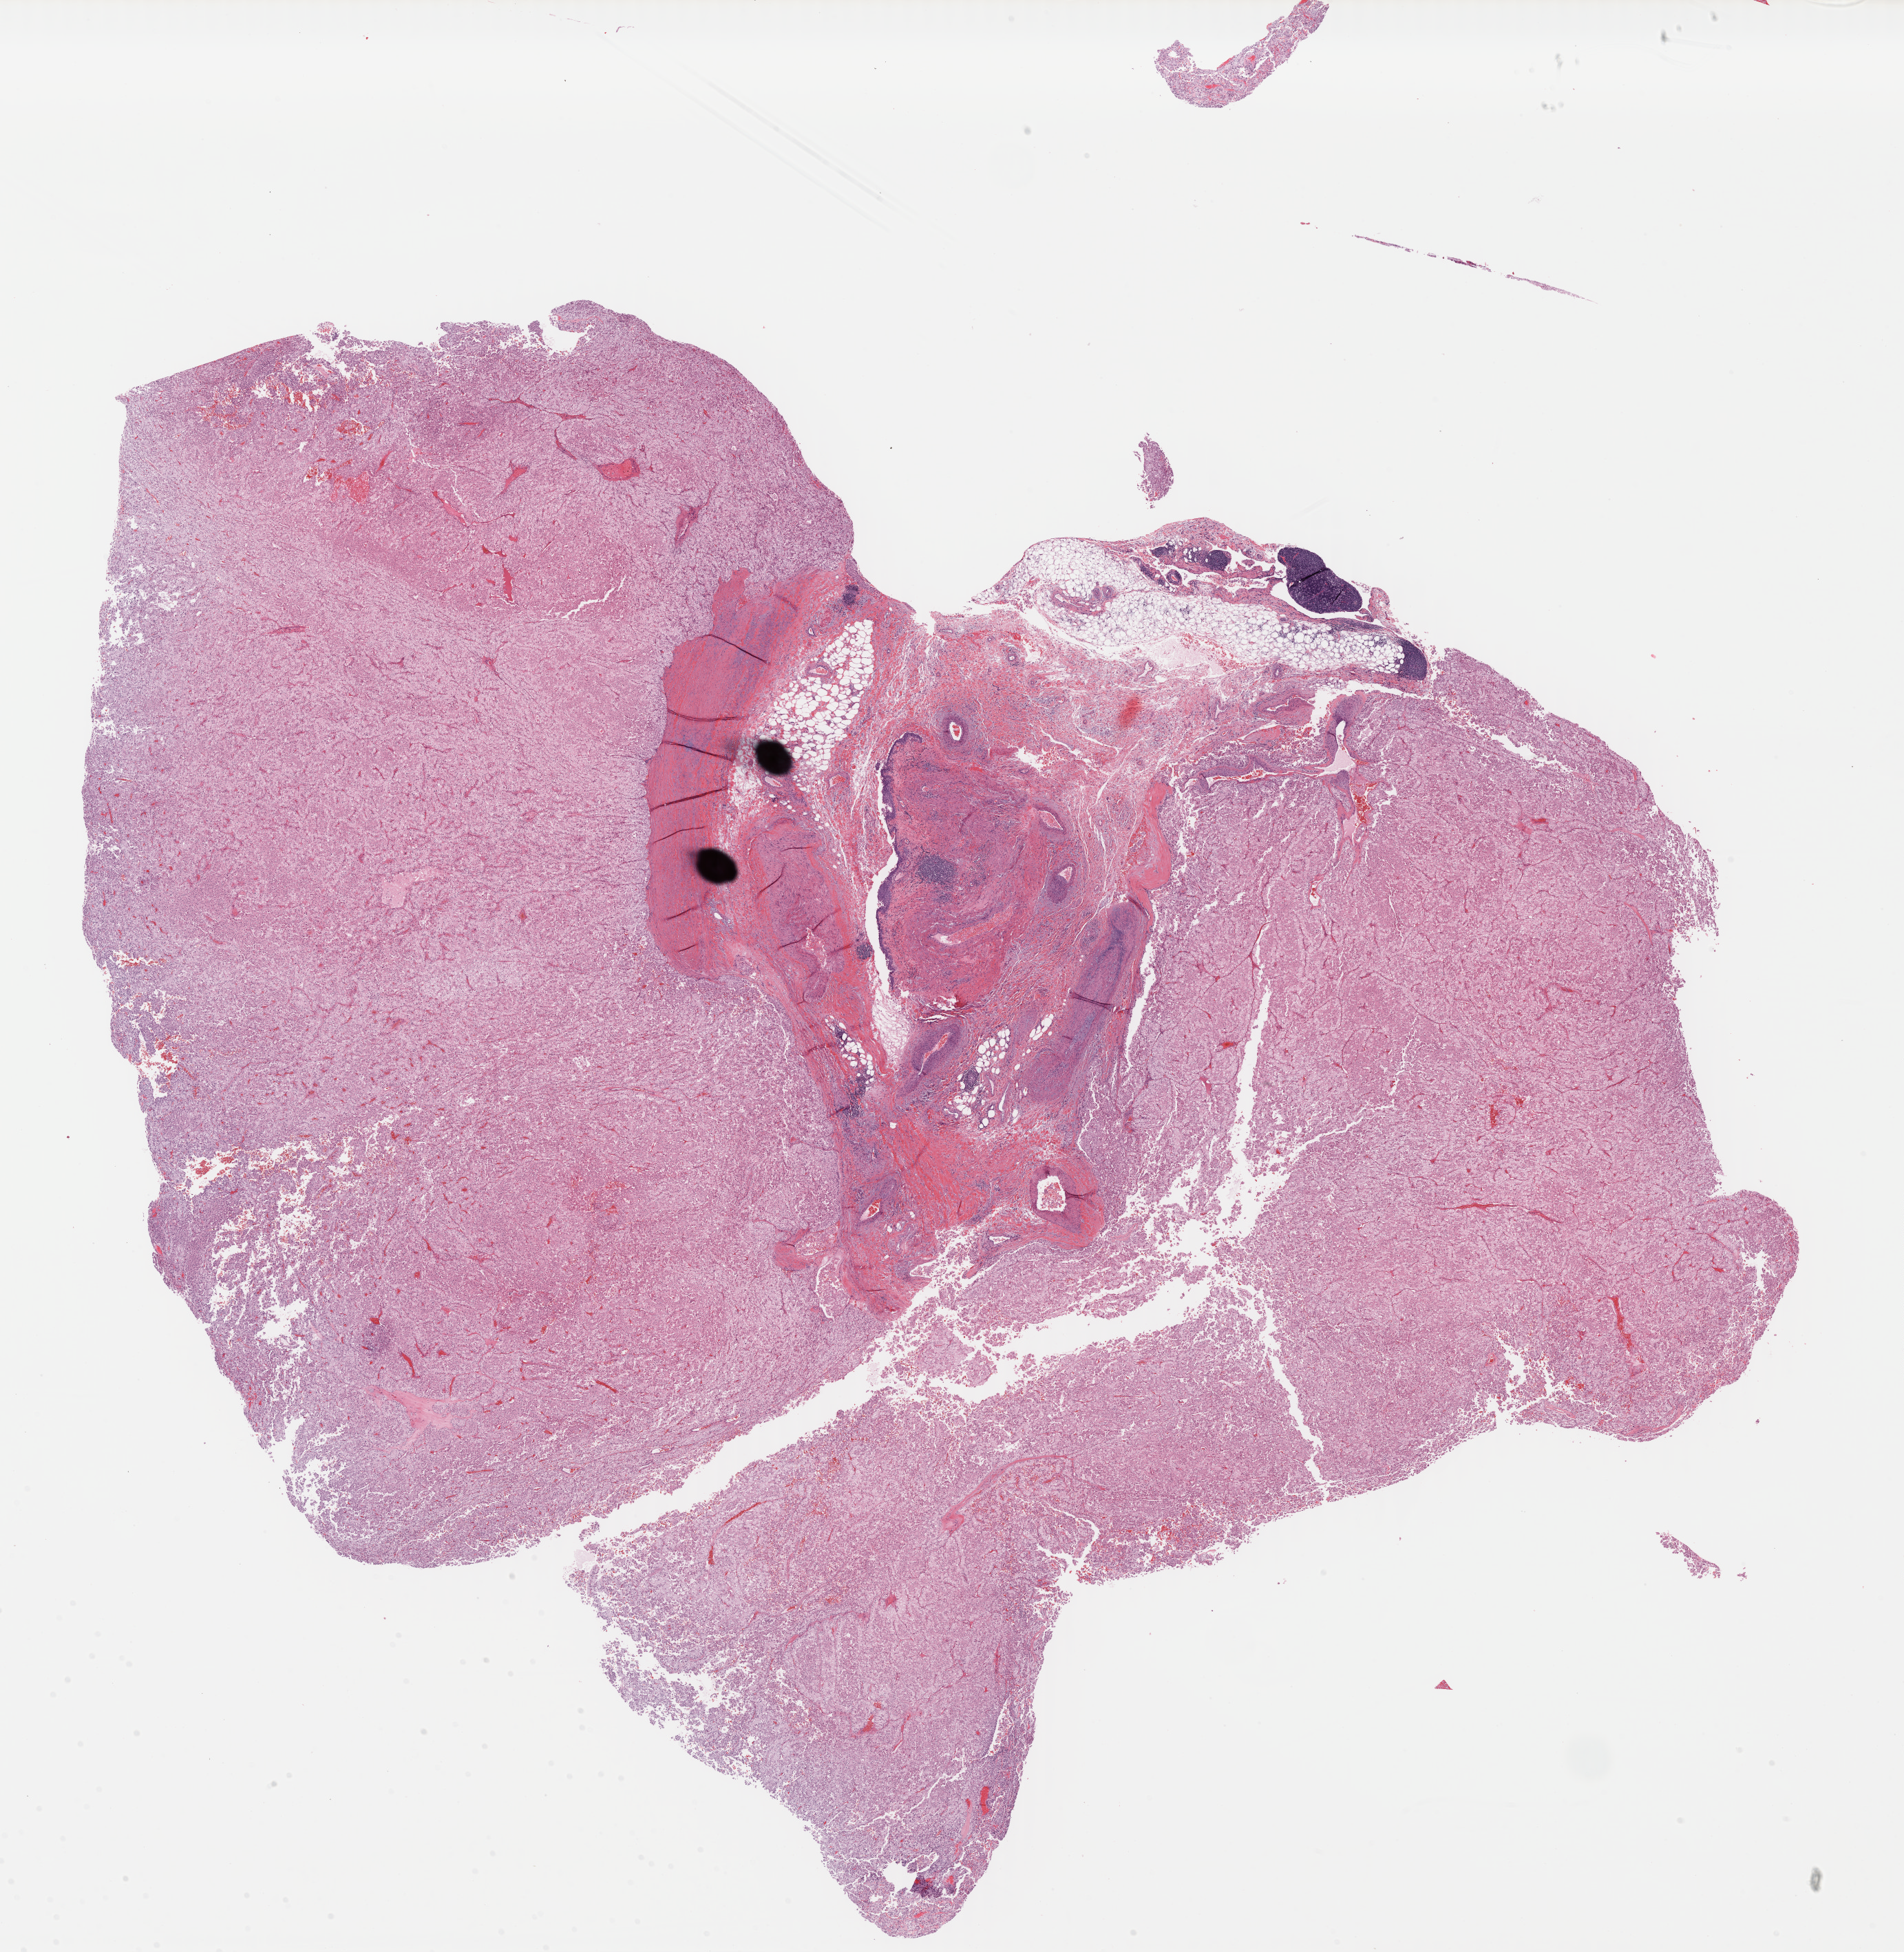
Whole-slide histology image, Hematoxylin and eosin (H&E) stained, whole scanned area (about 21.7 x 22.3 mm) shown as a low-resolution overview; FFPE section; primary tumour sample from the kidney. Female, age 50 years at initial diagnosis.
- histologic diagnosis: Renal cell carcinoma, chromophobe type
- TNM: T2 N0 M0
- AJCC pathologic stage: II
- laterality: left
- lymph nodes positive (case pathology): 0 of 9 examined